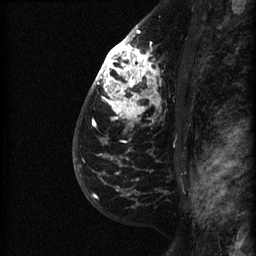
Breast MRI (dynamic contrast-enhanced), one sagittal slice. Slice 45 of 60 in the series (ordered by position). Dynamic contrast-enhanced series, image 2 of 3 at this slice position (ordered by acquisition). 1.5 T. TE 4.2 ms, TR 22.7 ms. 1.5 mm slice thickness. 256 × 256 image matrix. Female patient, age 48 years. From the clinical record (not read from this slice): setting: breast cancer imaged before/during neoadjuvant chemotherapy; receptor status: triple-negative.
Structures marked on this image (semi-automatic segmentation, software-assisted and operator-edited):
- analysis volume of interest (the breast-tissue region the enhancement analysis was run in; not a lesion): box from (x=89, y=27) to (x=188, y=180) px
- tumour enhancement mask (voxels above the 90 % enhancement threshold inside the analysis volume of interest): (x=95, y=30)–(x=157, y=156)